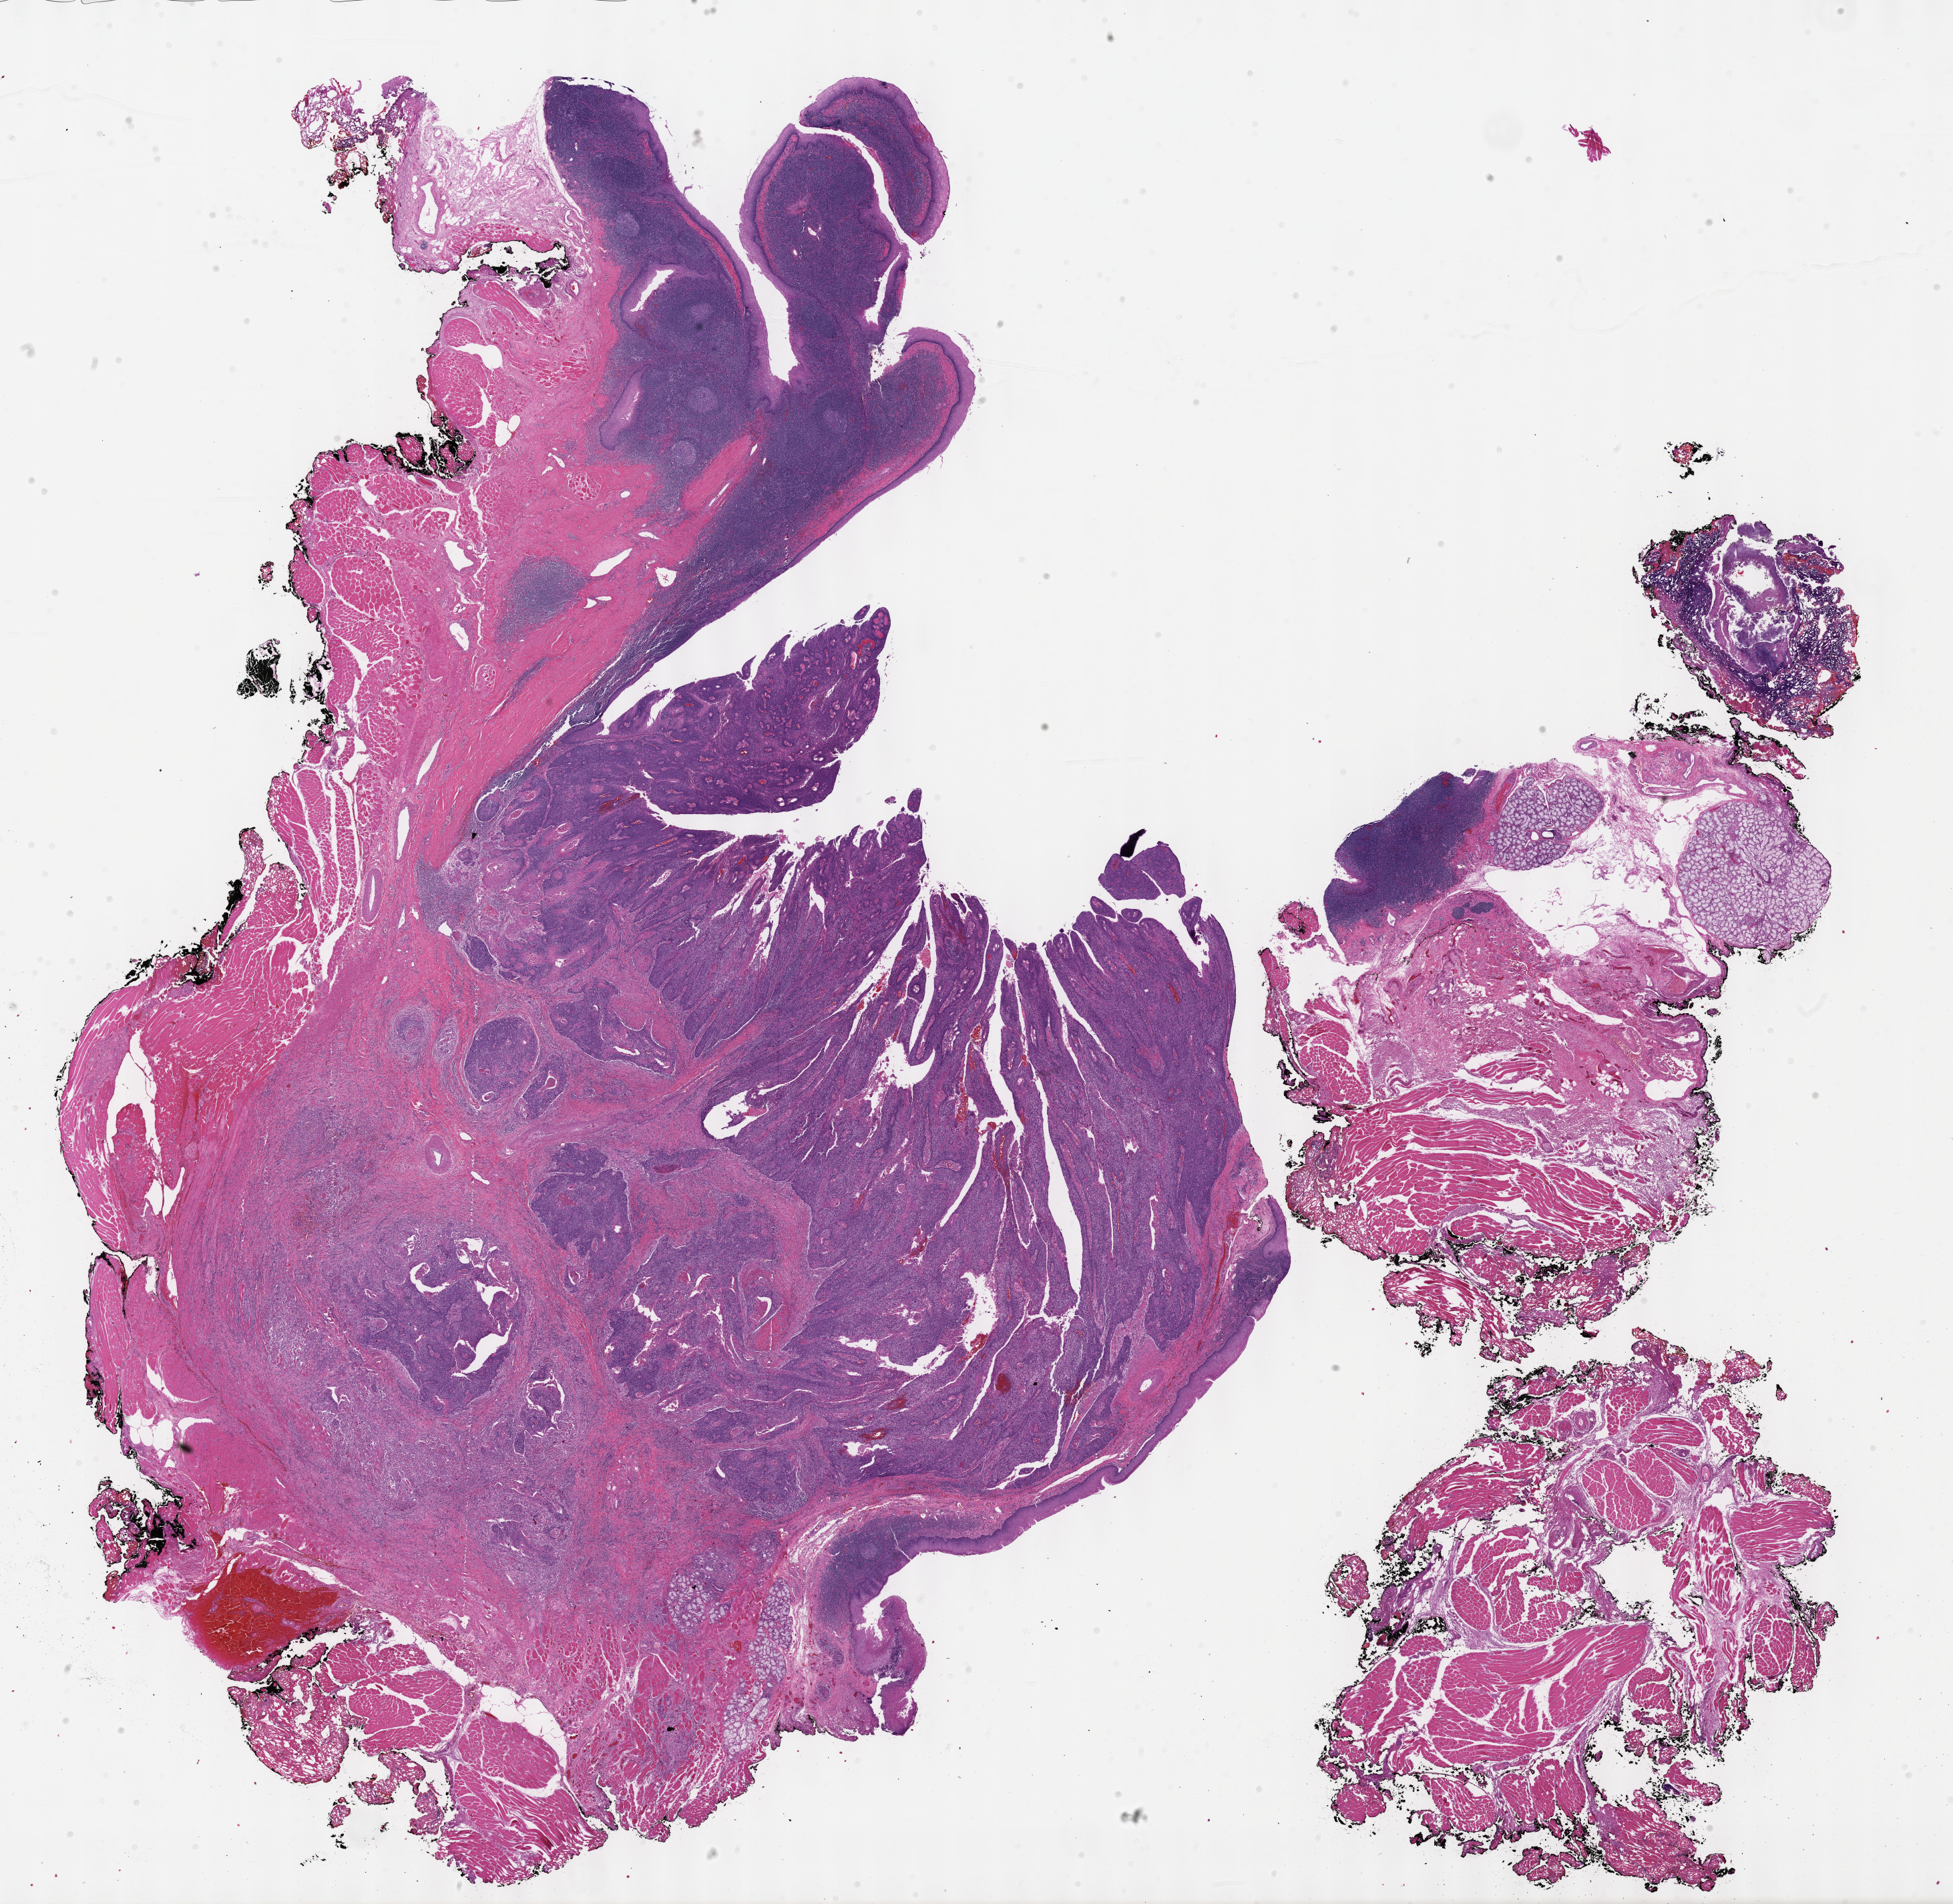
Digitized Hematoxylin and eosin (H&E) stained tissue section (whole slide) — whole scanned area (about 23.6 x 23.0 mm, from a 40x scan) shown as a low-resolution overview. Formalin-fixed paraffin-embedded (FFPE) diagnostic section. Primary tumour sample from the head and neck. Patient: male, age at initial diagnosis 52 years. Histologic grade: GX (grade cannot be assessed).
AJCC pathologic stage: III. TNM: T1 N2 MX. Pathologic diagnosis: Squamous cell carcinoma, NOS (tonsil, NOS). Laterality: left.